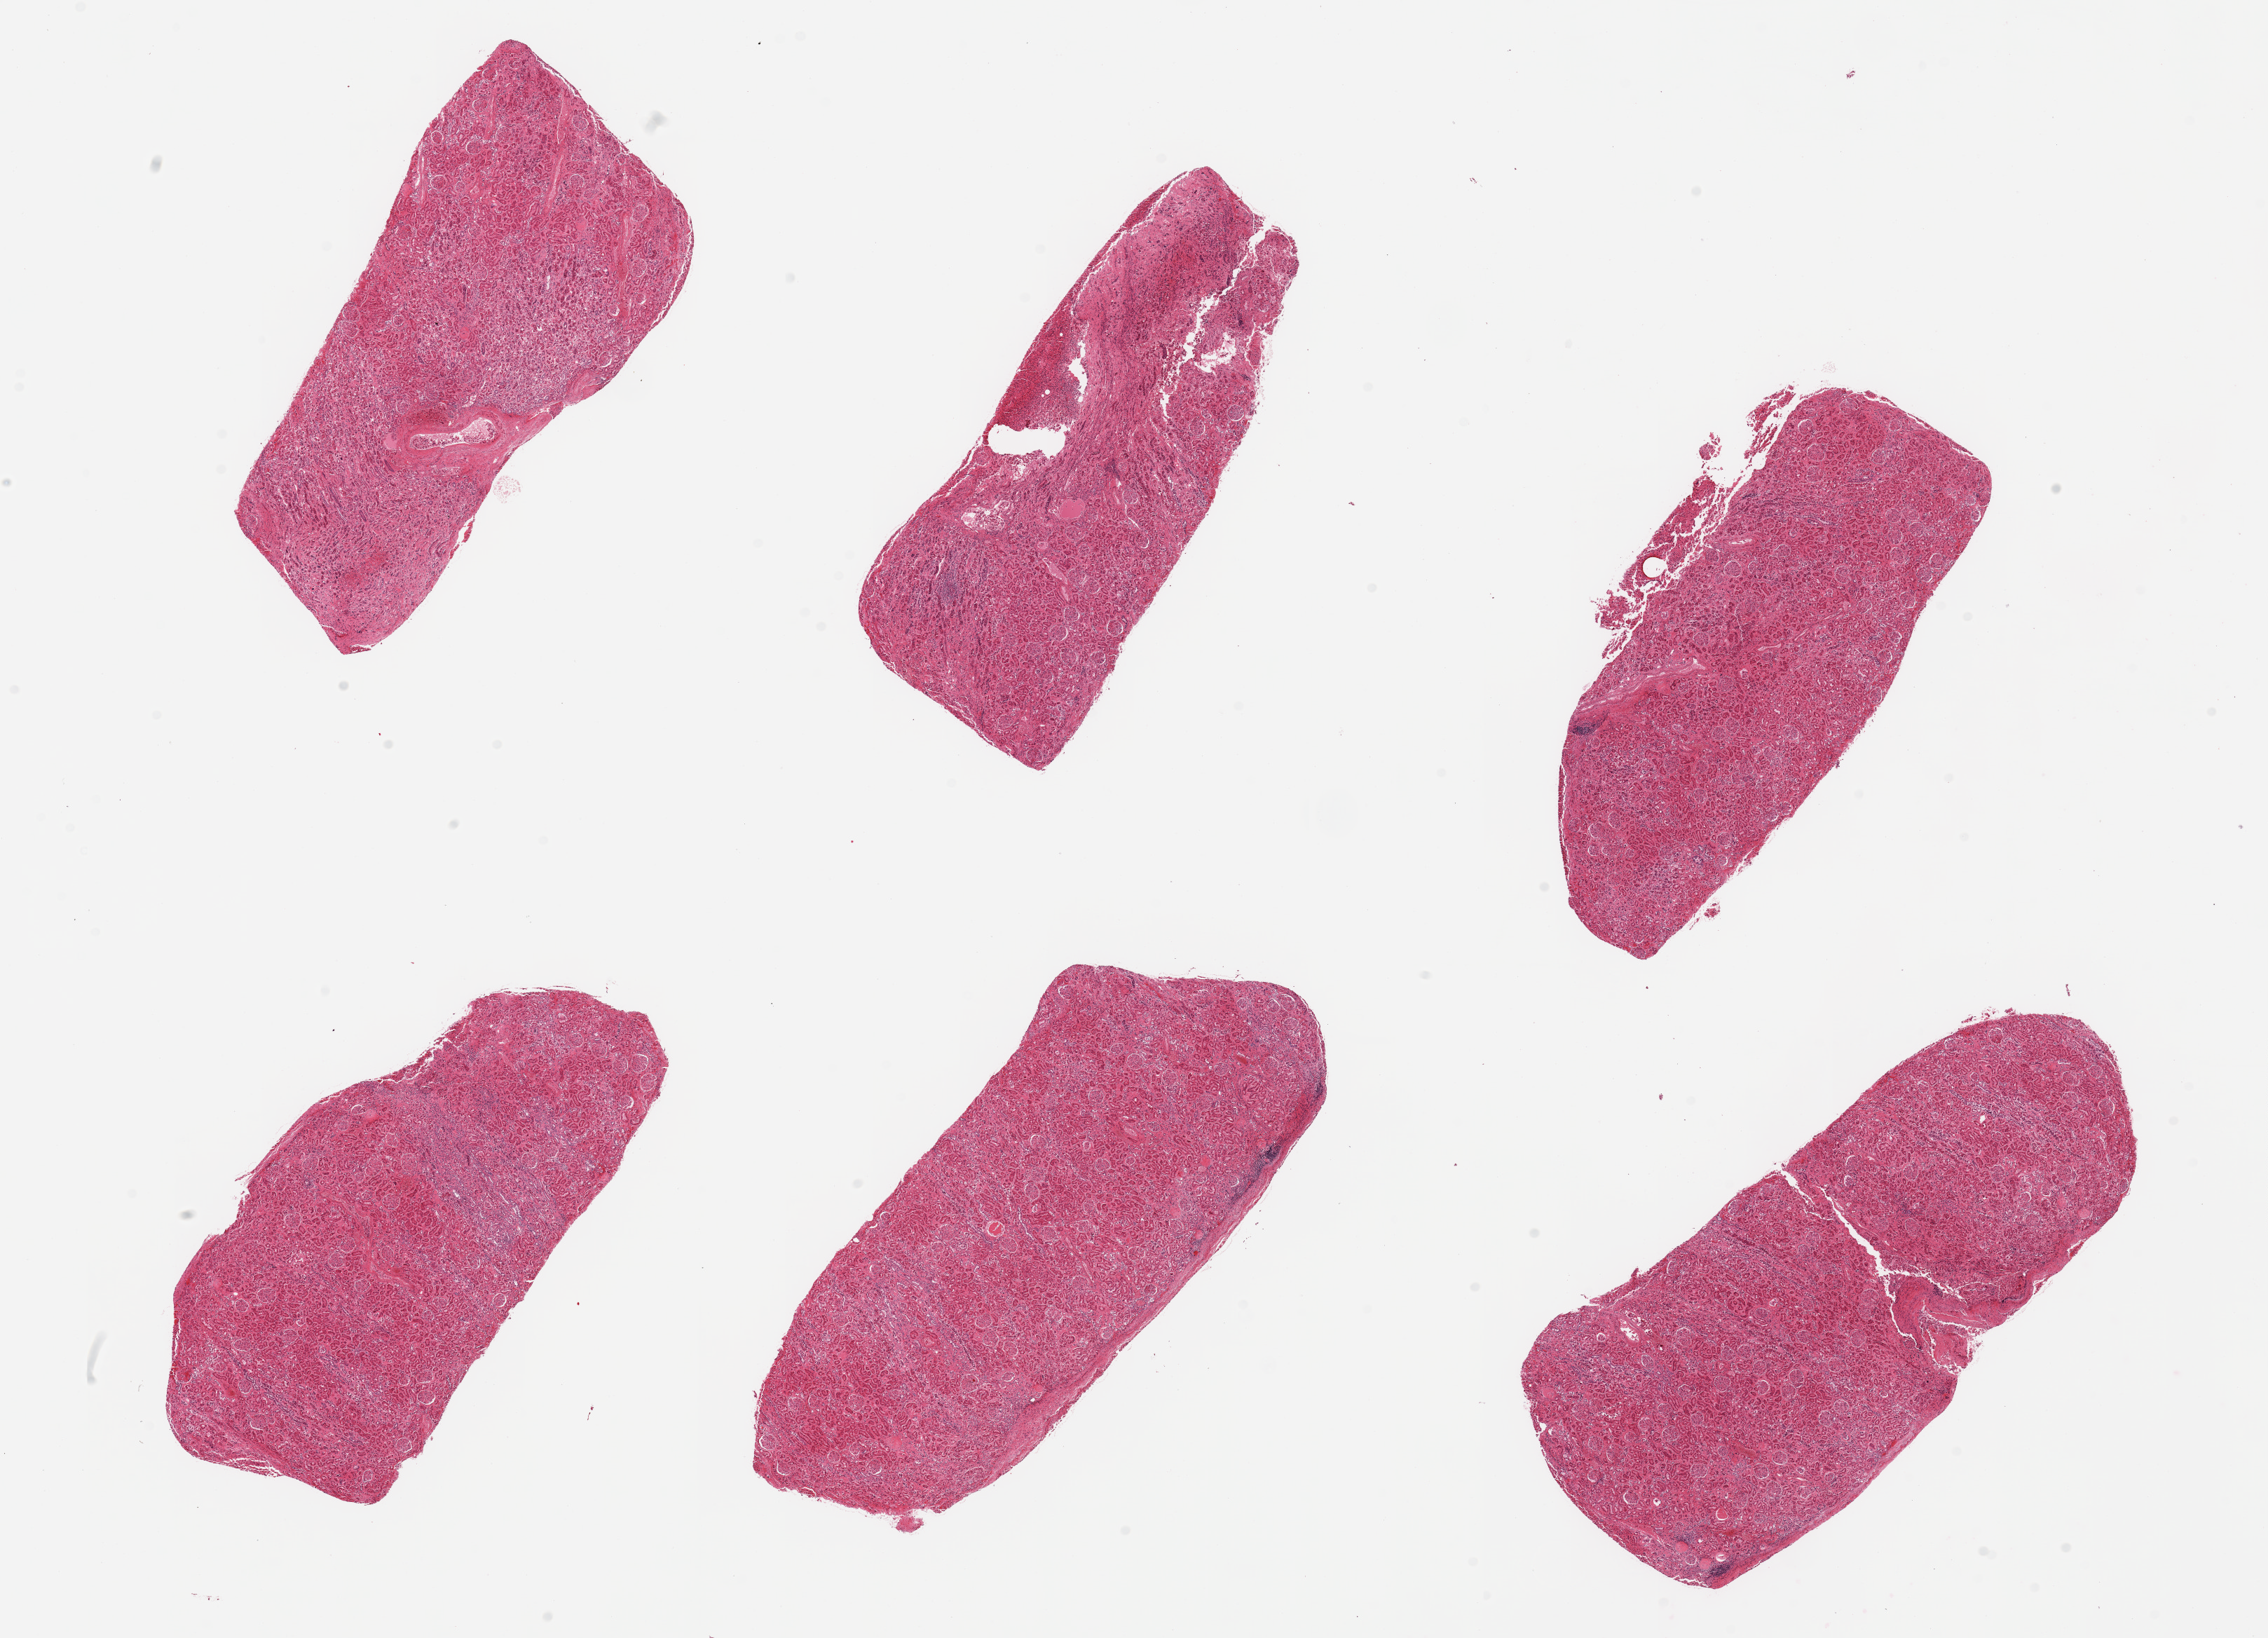
Digitized haematoxylin and eosin-stained section, shown as a low-resolution overview of the whole scanned area (about 25.6 x 18.5 mm, acquisition: 20x scan); PAXgene-fixed, paraffin-embedded tissue; target tissue: renal cortex; donor tissue sample. Donor: male.
Pathologist's review note for this sample: 6 pieces, glomeruli present, badly autolyzed.